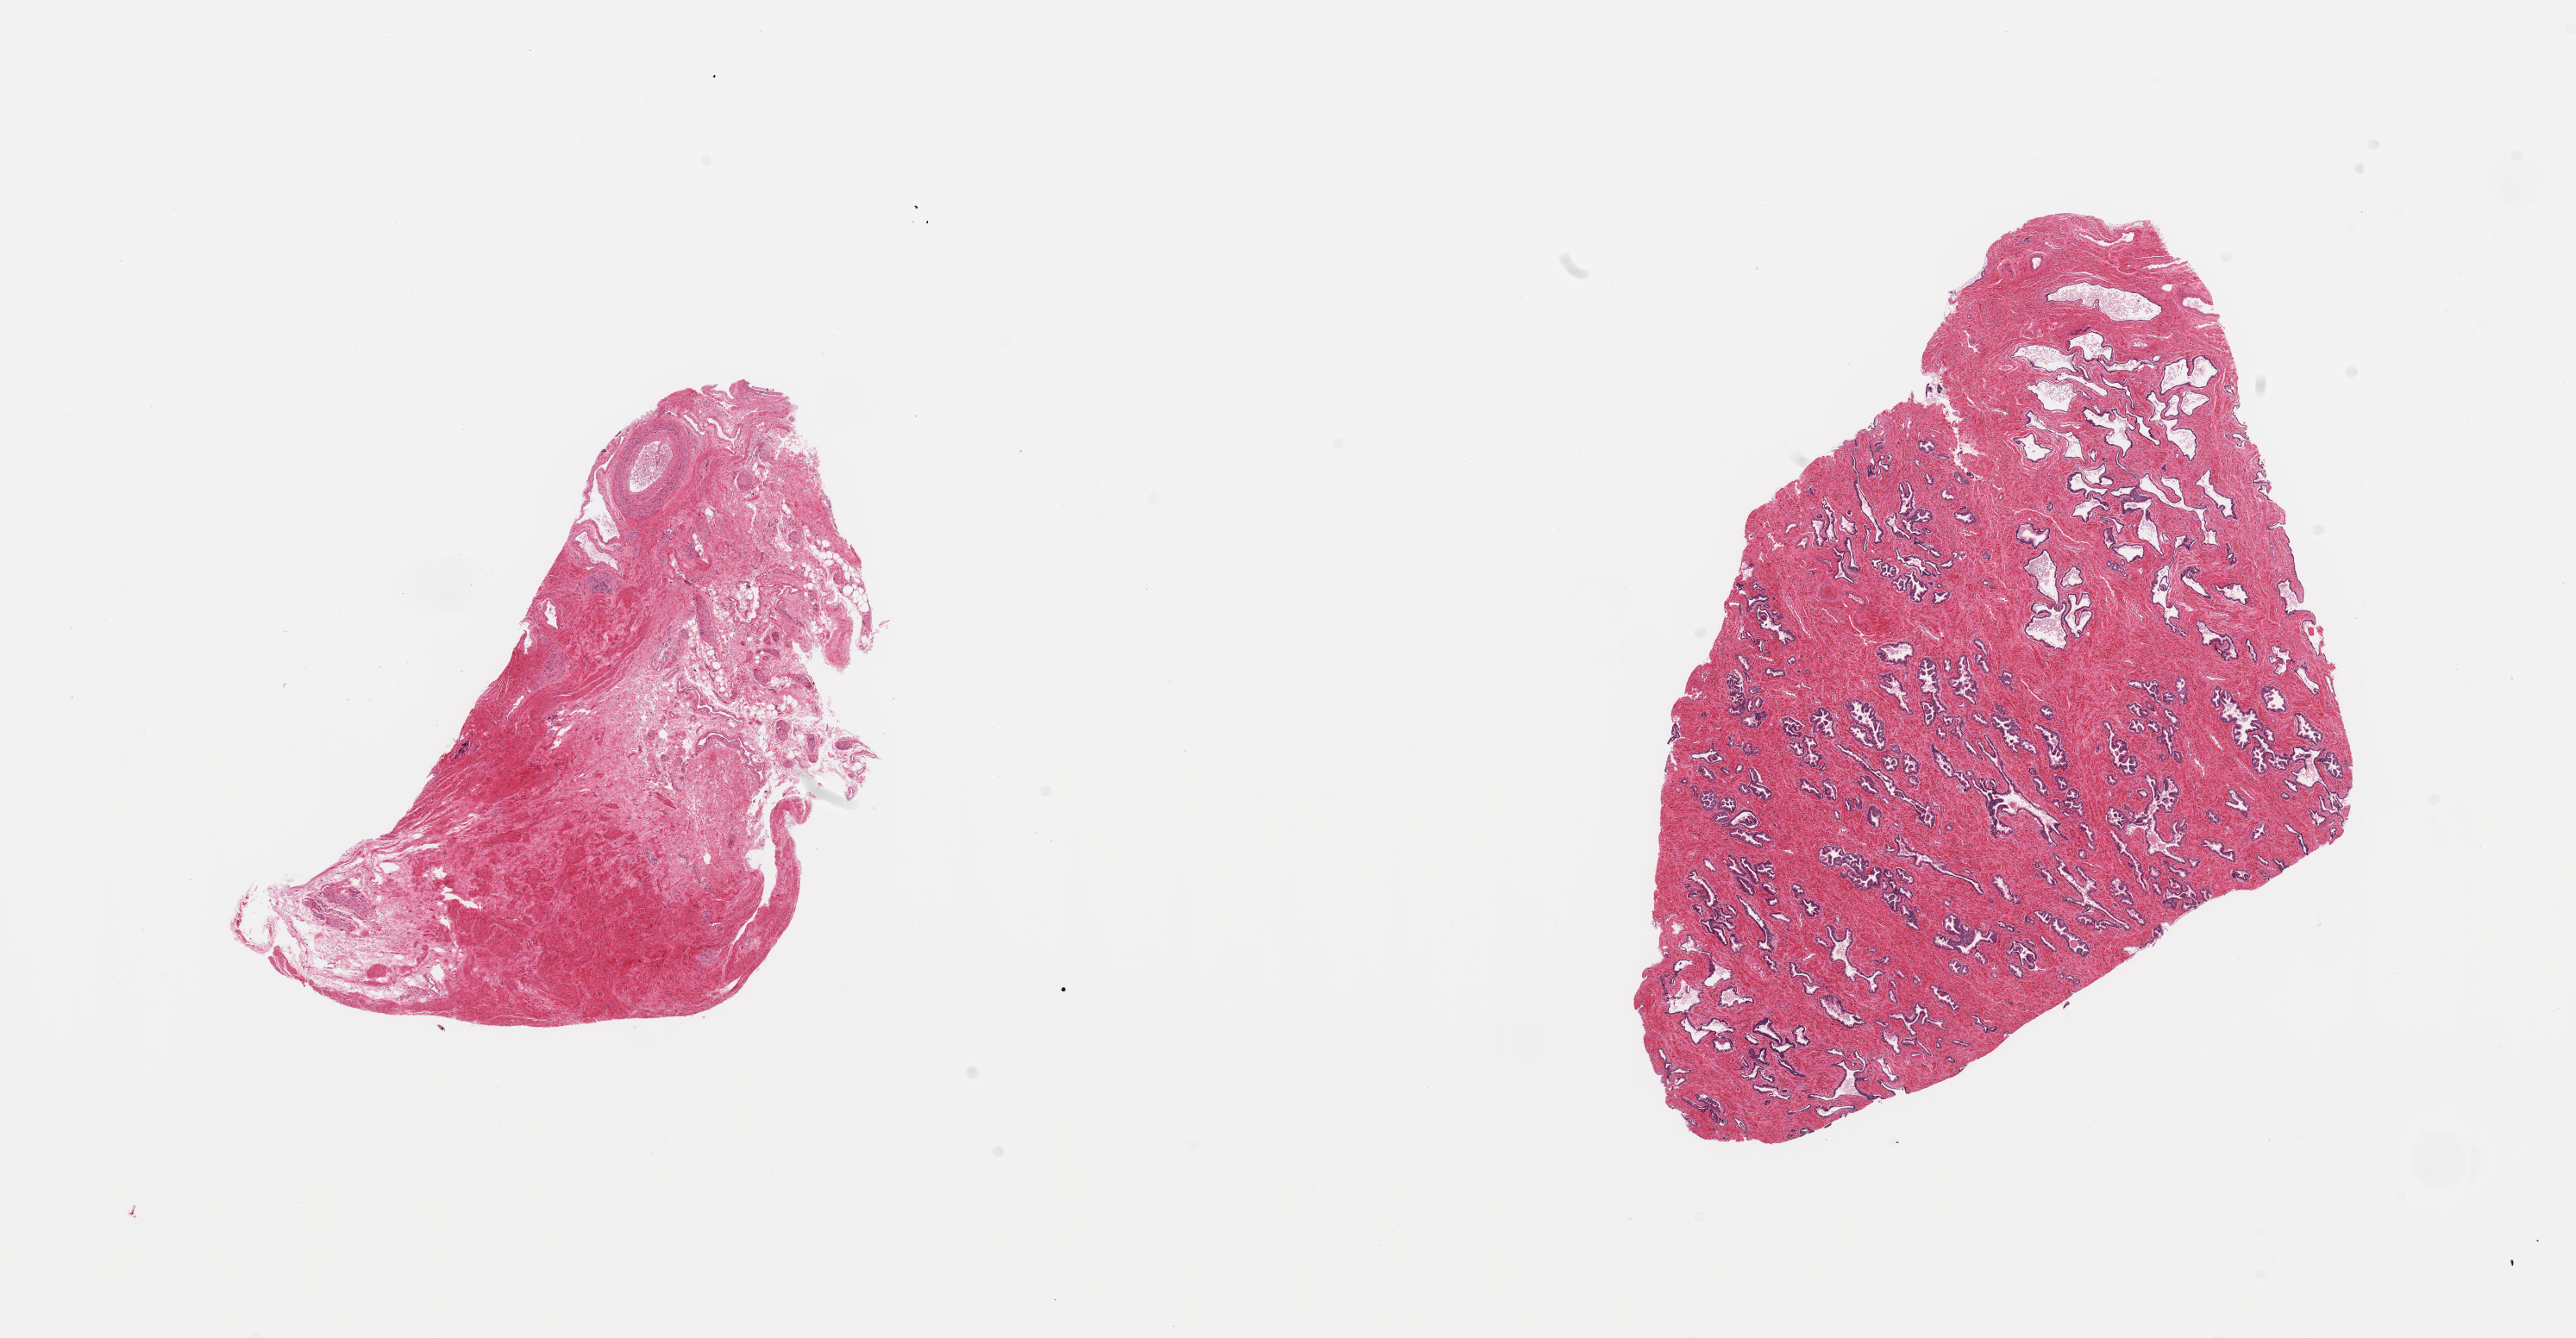
H&E whole-slide image, brightfield, low-resolution overview of the scanned area, about 23.6 x 12.3 mm, PAXgene-fixed, paraffin-embedded tissue, sampled site (target tissue): prostate, donor tissue sample.
- review note (as recorded): 2 pieces; 1 piece contains stroma and muscle without prostatic tissue